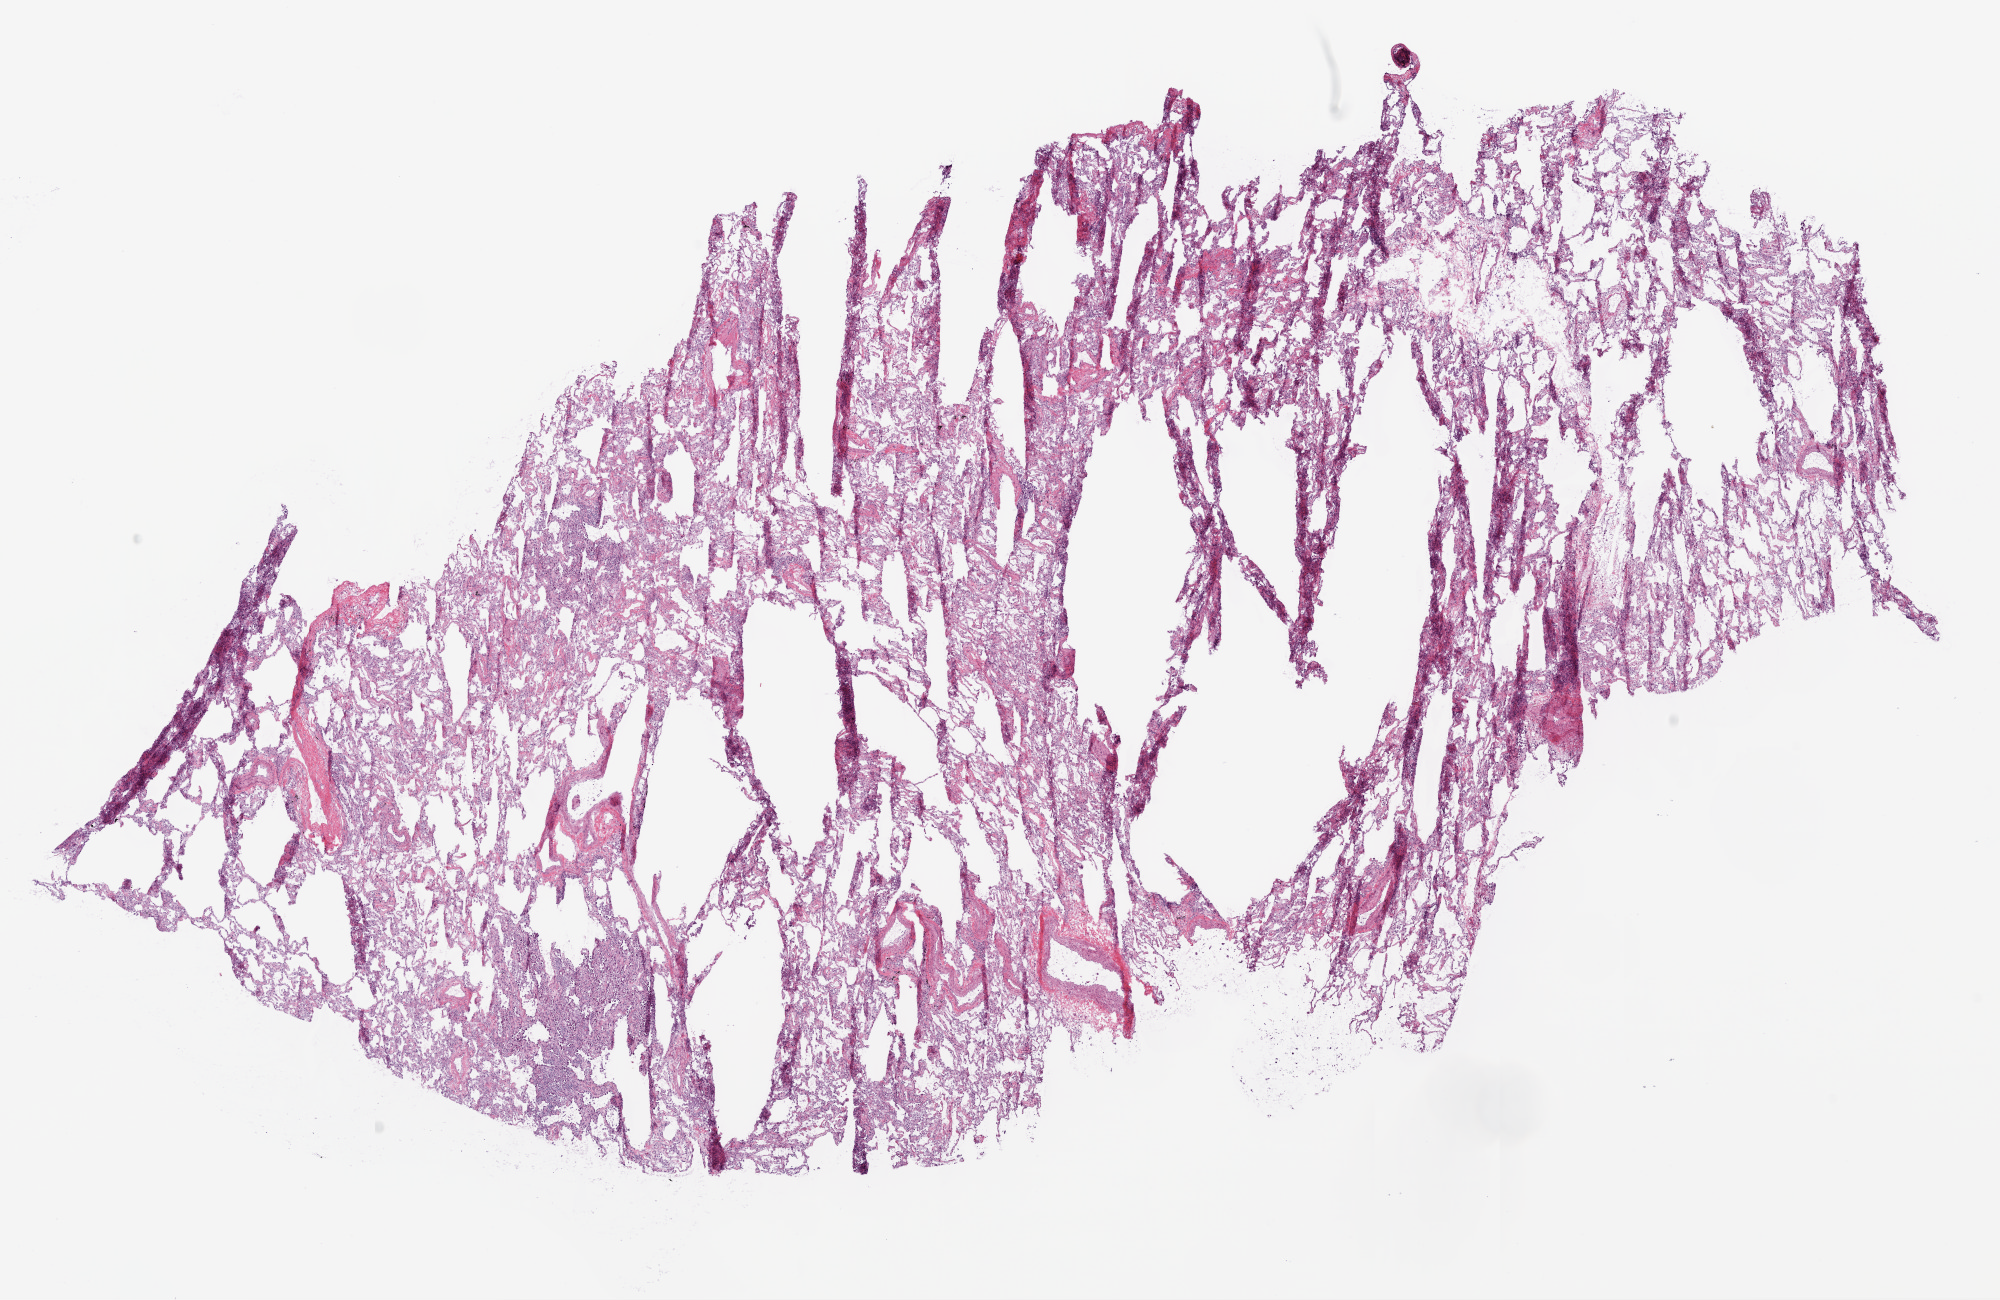
Digitized H&E tissue section (whole slide), low-resolution overview of the scanned area, about 16.0 x 10.4 mm, frozen section from the bottom of the tissue portion, sample: solid tissue normal (non-tumour tissue), lung. Female, age 60 years at initial diagnosis.
This section: solid tissue normal (non-tumour) sample from the same patient. Patient diagnosis: Adenocarcinoma, NOS (upper lobe, lung).